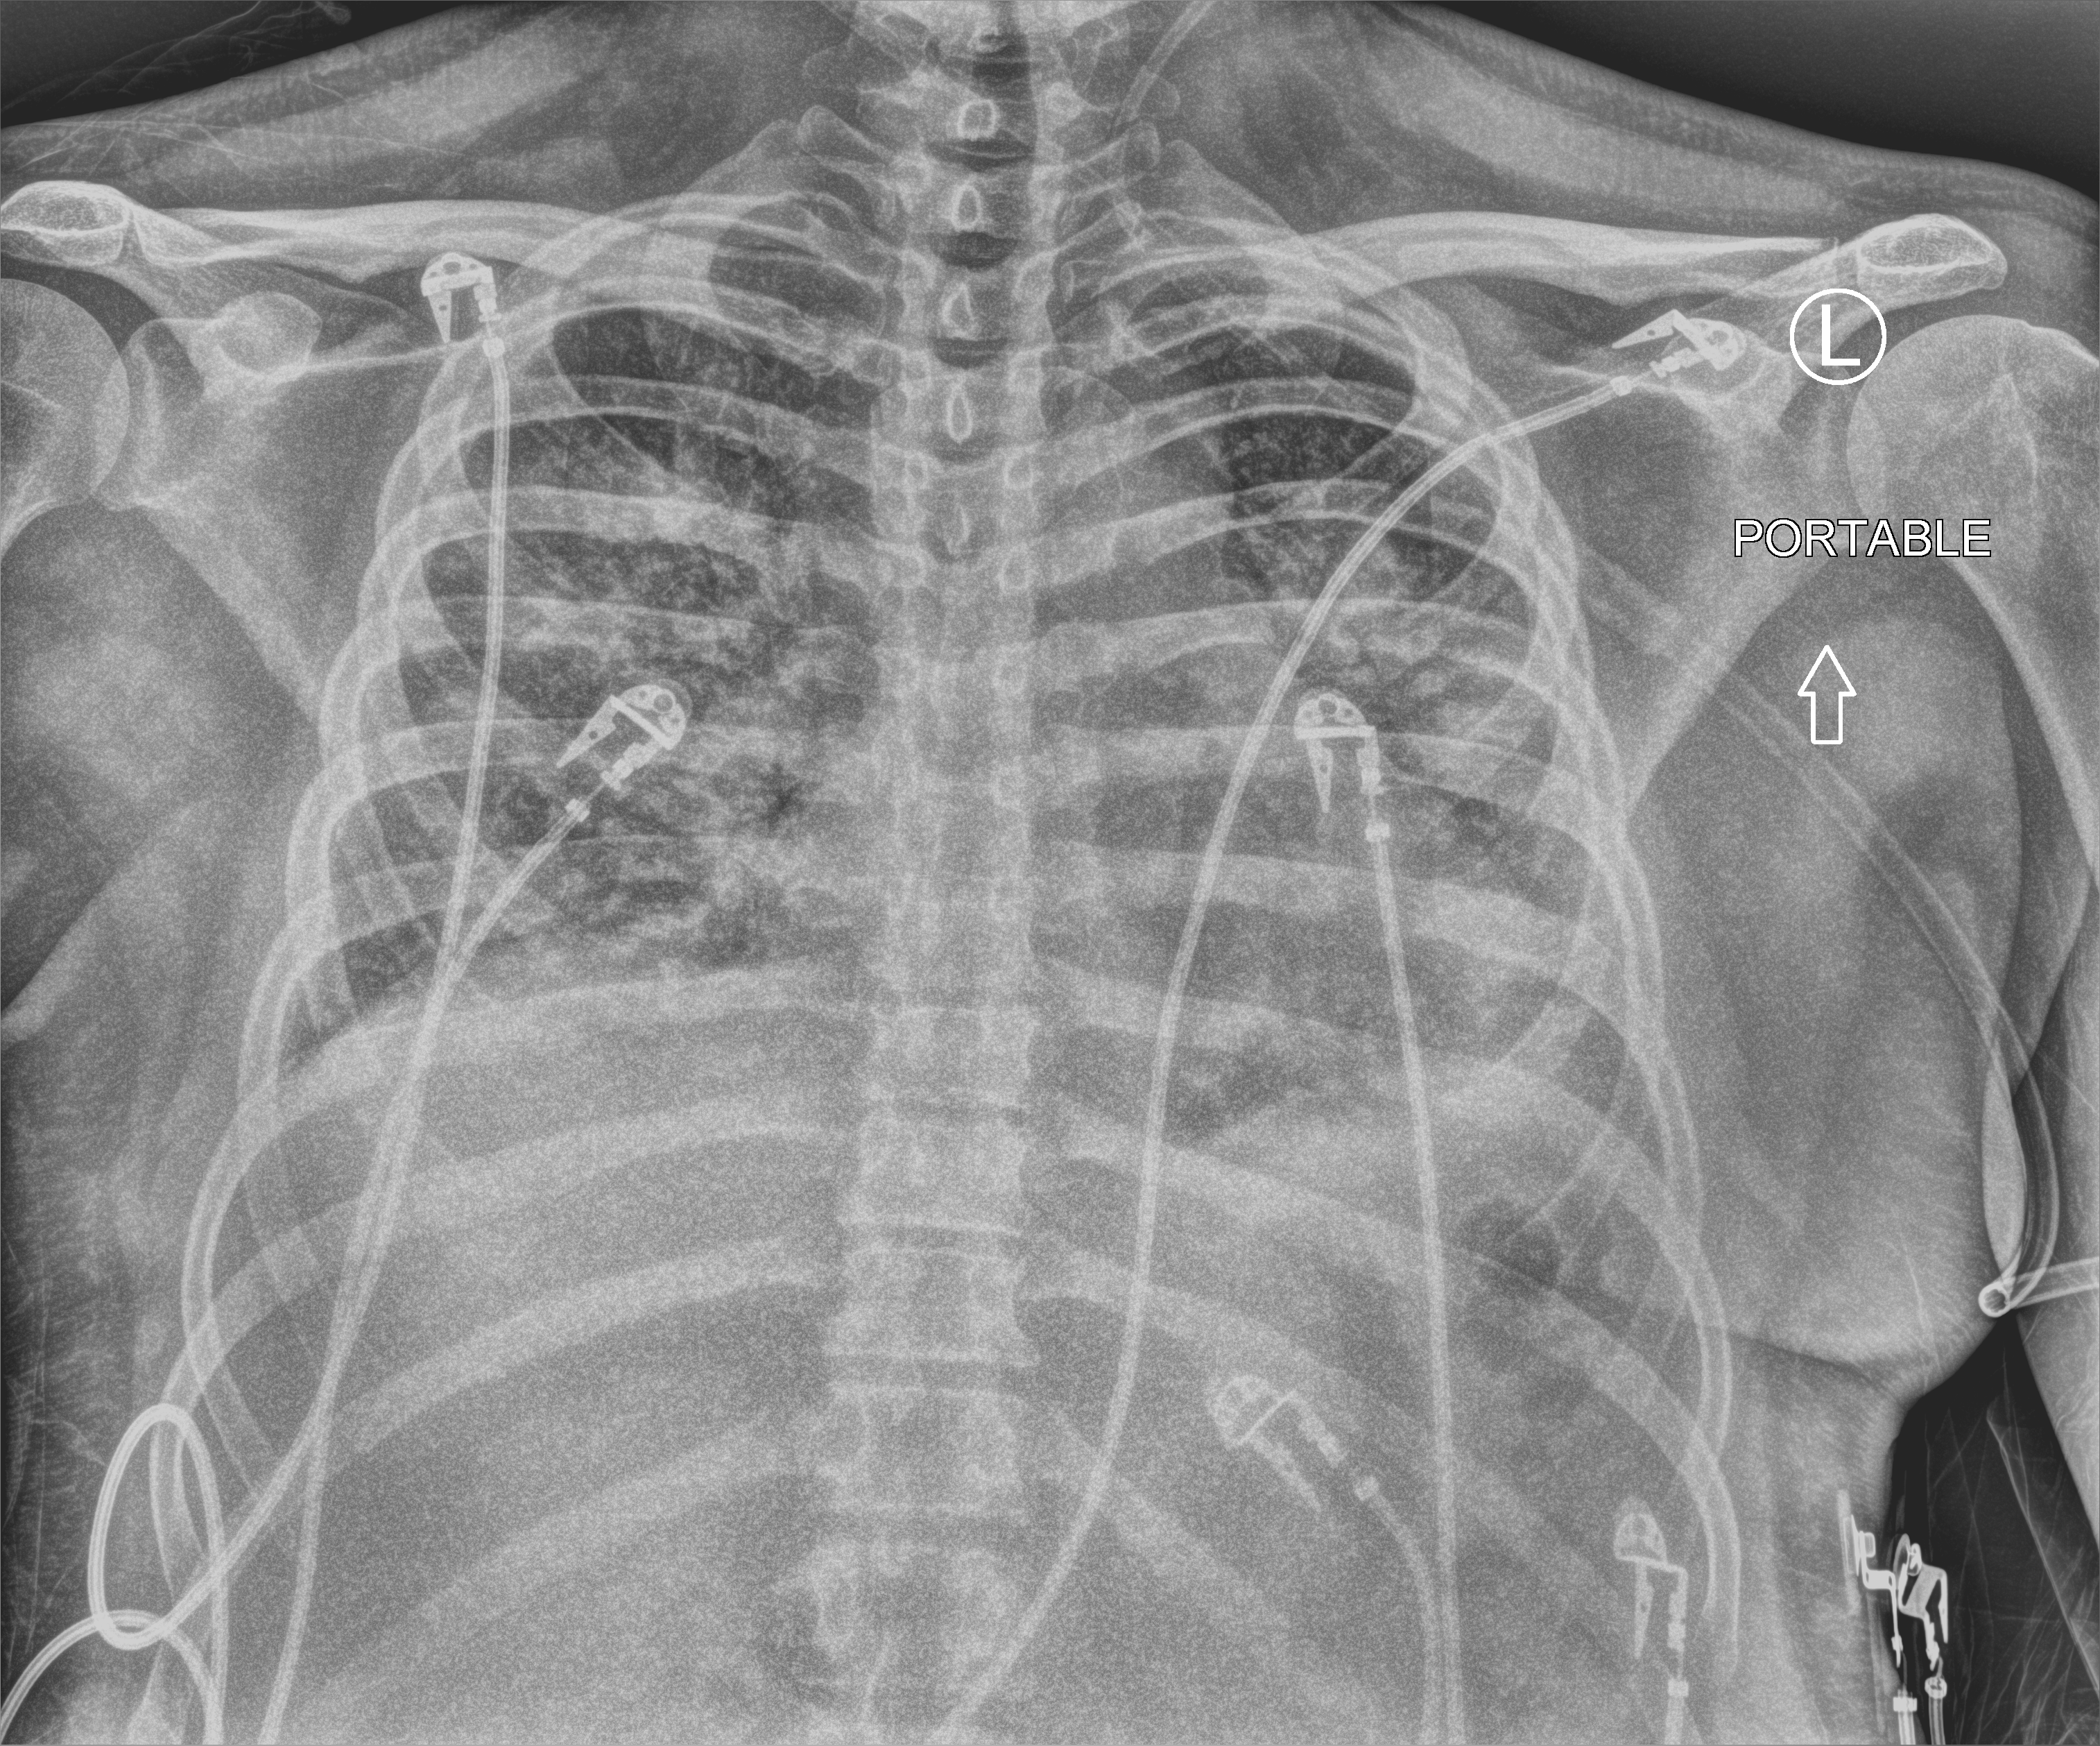
Portable chest radiograph, anteroposterior (AP) projection. Male patient hospitalised with COVID-19, age 18–59 years.
From the hospital-stay record, not from the radiograph (when in the stay this image was taken is not recorded): mechanically ventilated during this hospital stay: no; admitted to intensive care during this hospital stay: no.